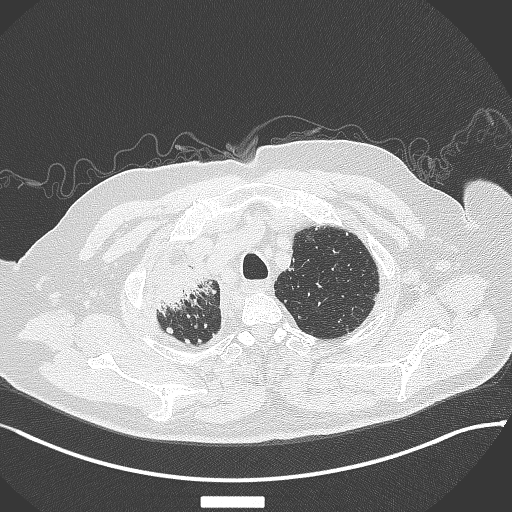
Chest CT, one axial slice. Position 320 of 384 along the scan axis. Lung window (W 1500 / L -600 HU). 512 × 512 image matrix, field of view 400 × 400 mm. Male patient, age 69 years. Case-level facts recorded for this patient, not image findings: clinical TNM (as recorded): T4 N3 M1.
Annotated regions visible in this slice (rectangle marked by the reading radiologist):
- lung tumour (recorded histology: adenocarcinoma): bounding box [x1, y1, x2, y2] px = [150, 252, 214, 313]